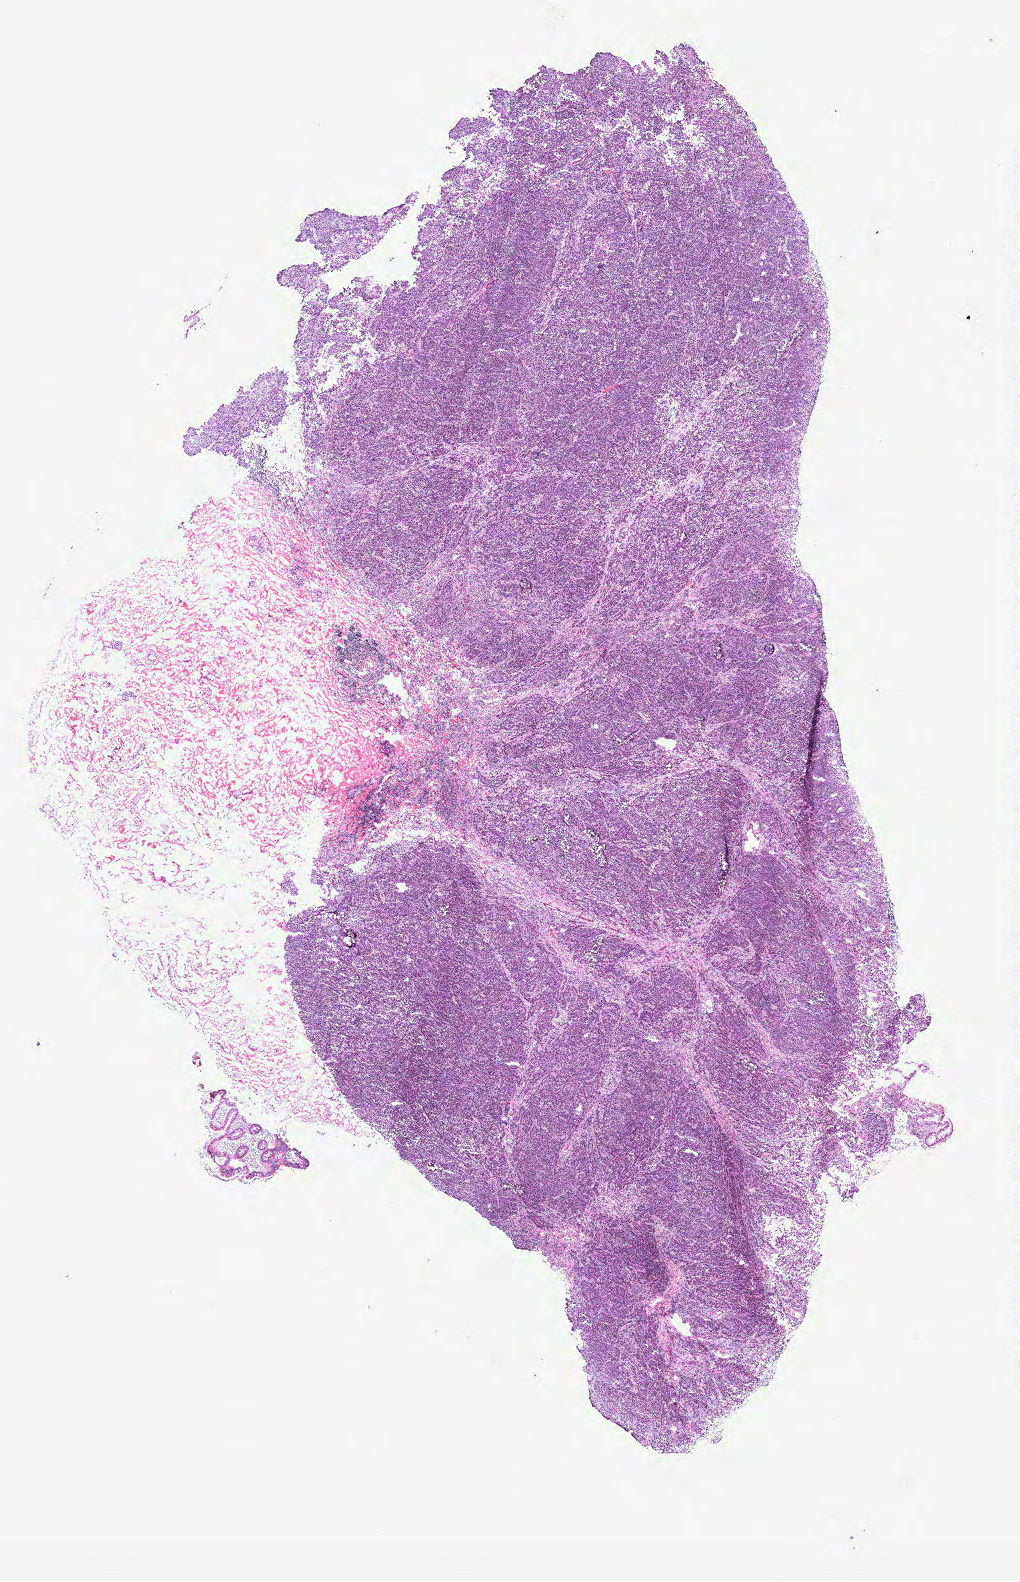
H&E-stained whole-slide image, a low-resolution overview of the entire scanned area, about 8.2 x 12.7 mm (slide scanned at 40x); colon, tissue type not recorded.
Patient diagnosis (cohort enrolment): colon cancer (colon).